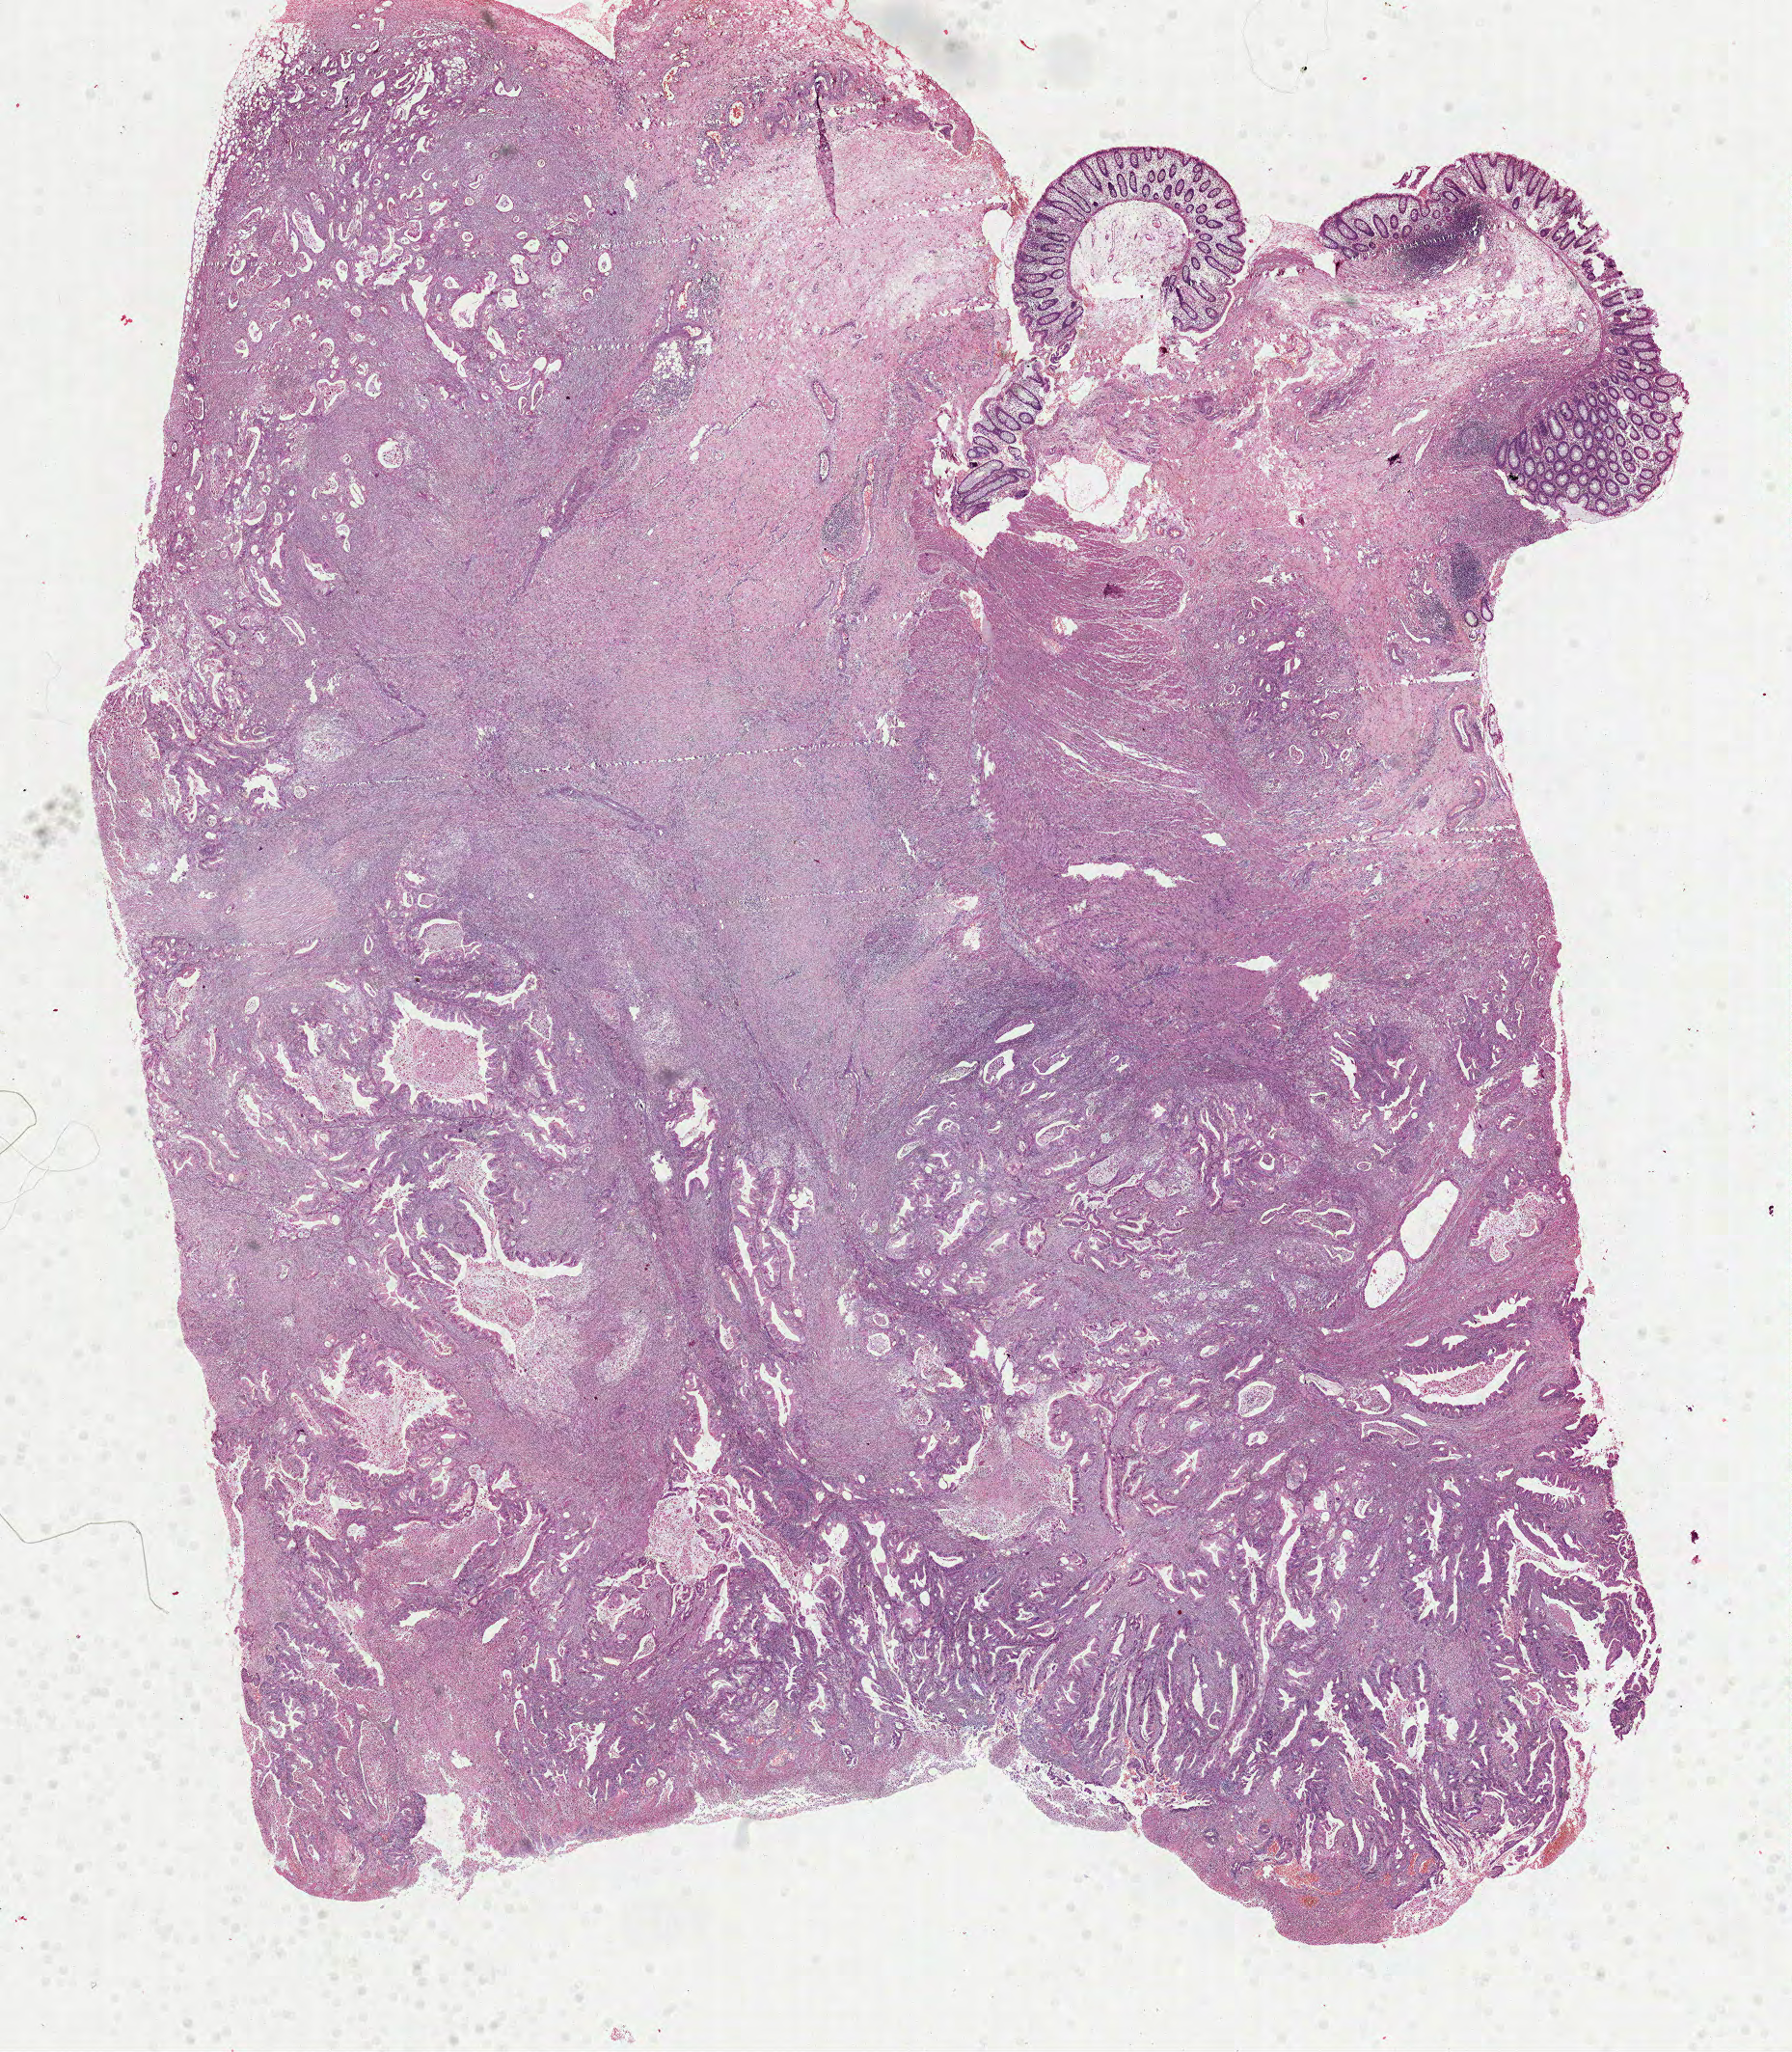
Digitized Hematoxylin and eosin (H&E) stained tissue section (whole slide), whole scanned area (about 15.0 x 17.2 mm) shown as a low-resolution overview, formalin-fixed paraffin-embedded (FFPE) diagnostic section, colon, primary tumour sample. Patient: male, age at initial diagnosis 45 years.
Diagnosis: Adenocarcinoma, NOS.